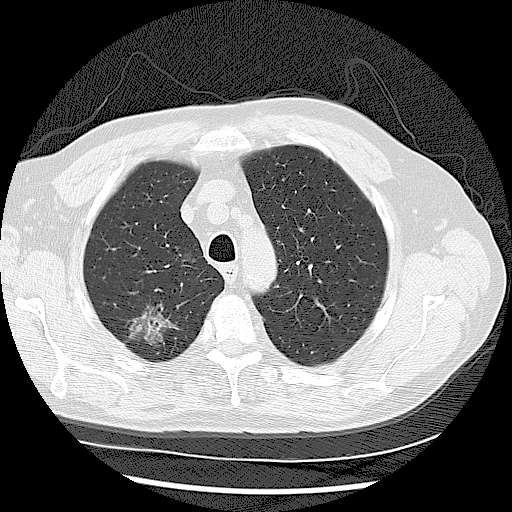
Low-dose screening chest CT, one axial slice. Position 92 of 122 along the scan axis. Reconstruction kernel LUNG. 120 kVp. Lung window (W 1500 / L -600 HU). 2.5 mm slice thickness. 512 × 512 image matrix.
Outlined on this slice (expert manual segmentation):
- lesion 1 (tumor, upper lobe of right lung): bounding box <130,305,177,344> (left, top, right, bottom; pixels)